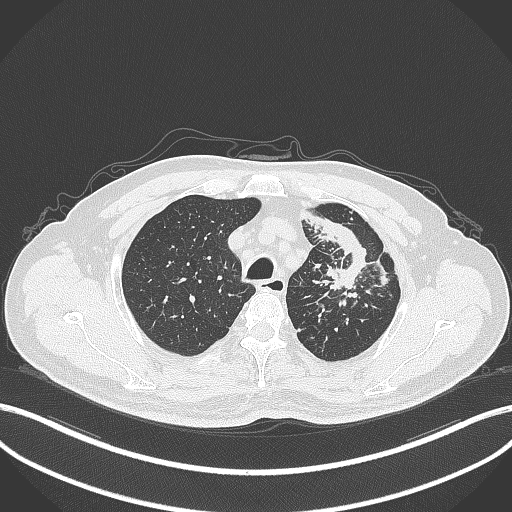
Chest CT, one axial slice; slice 288 of 386 in the series (ordered by position); reconstruction kernel B70f; 120 kVp; lung window (W 1500 / L -600 HU); 1 mm slice thickness; 512 × 512 image matrix. Patient: male, 69 years. Case-level facts recorded for this patient, not image findings: clinical TNM (as recorded): T2a N2 M0; histopathological grade: G2-3.
Annotated regions visible in this slice (bounding box drawn by a radiologist):
- lung tumour (recorded histology: adenocarcinoma): bounding box (x1, y1, x2, y2) in pixels: (310, 213, 375, 293)